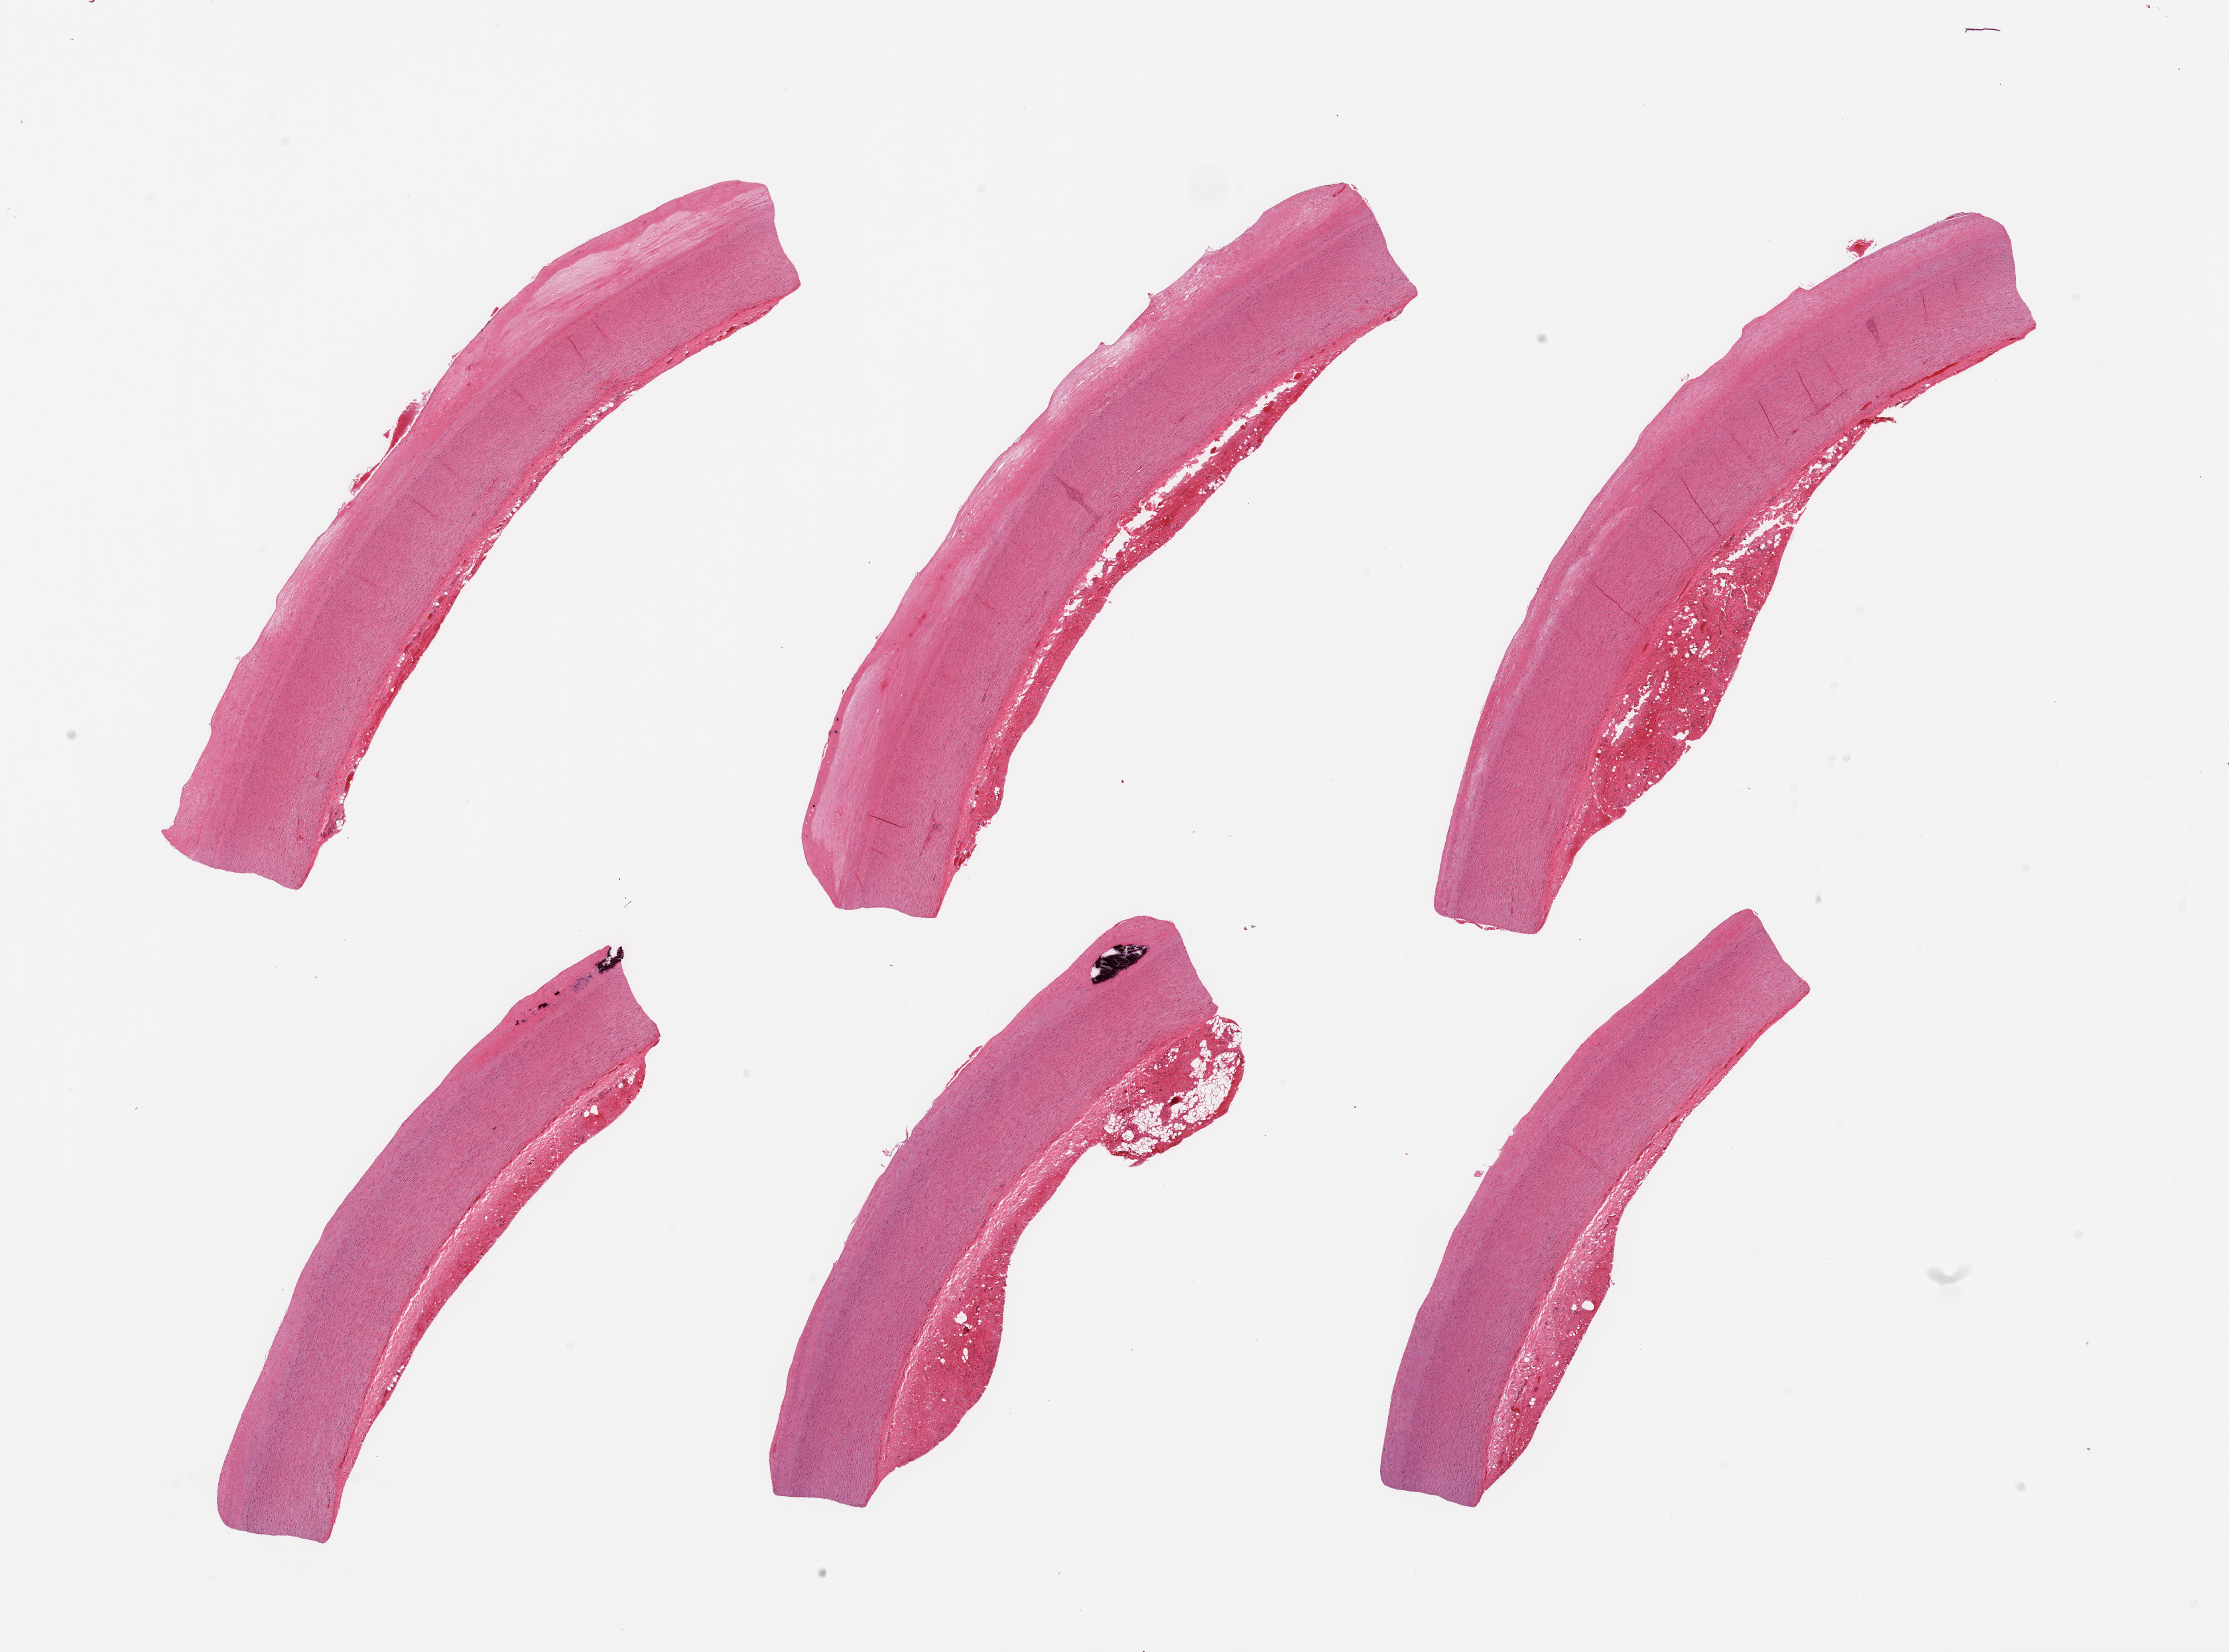
H&E whole-slide image, whole scanned area (about 26.6 x 19.7 mm, acquisition: 20x scan) shown as a low-resolution overview; PAXgene-fixed, paraffin-embedded tissue; target tissue: aorta; tissue donor sample. Male donor.
Review note (as recorded): 6 pieces; slight fibrous intimal thickening; no plaques; small calcific deposit in 2 pieces; generally well trimmed.